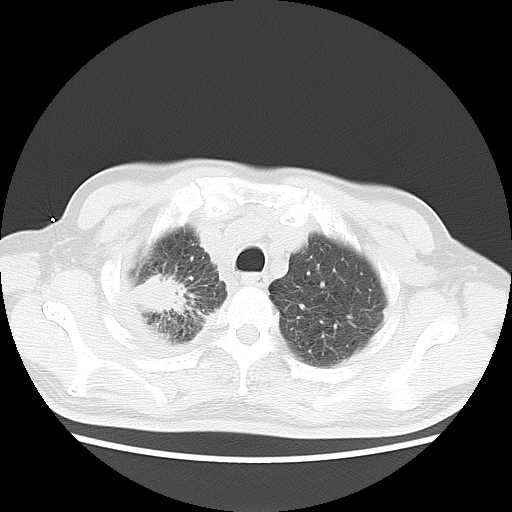
Chest CT, one axial slice. Position 16 of 20 along the scan axis. 120 kVp. Lung window (W 1500 / L -600 HU). 5 mm slice thickness. 512 × 512 image matrix, field of view 350 × 350 mm. Male patient, age 75 years. Case-level facts recorded for this patient, not image findings: clinical TNM (as recorded): T1c N1 M1.
Annotated regions visible in this slice (rectangle marked by the reading radiologist):
- lung tumour (recorded histology: adenocarcinoma): box from (x=132, y=269) to (x=190, y=320) px